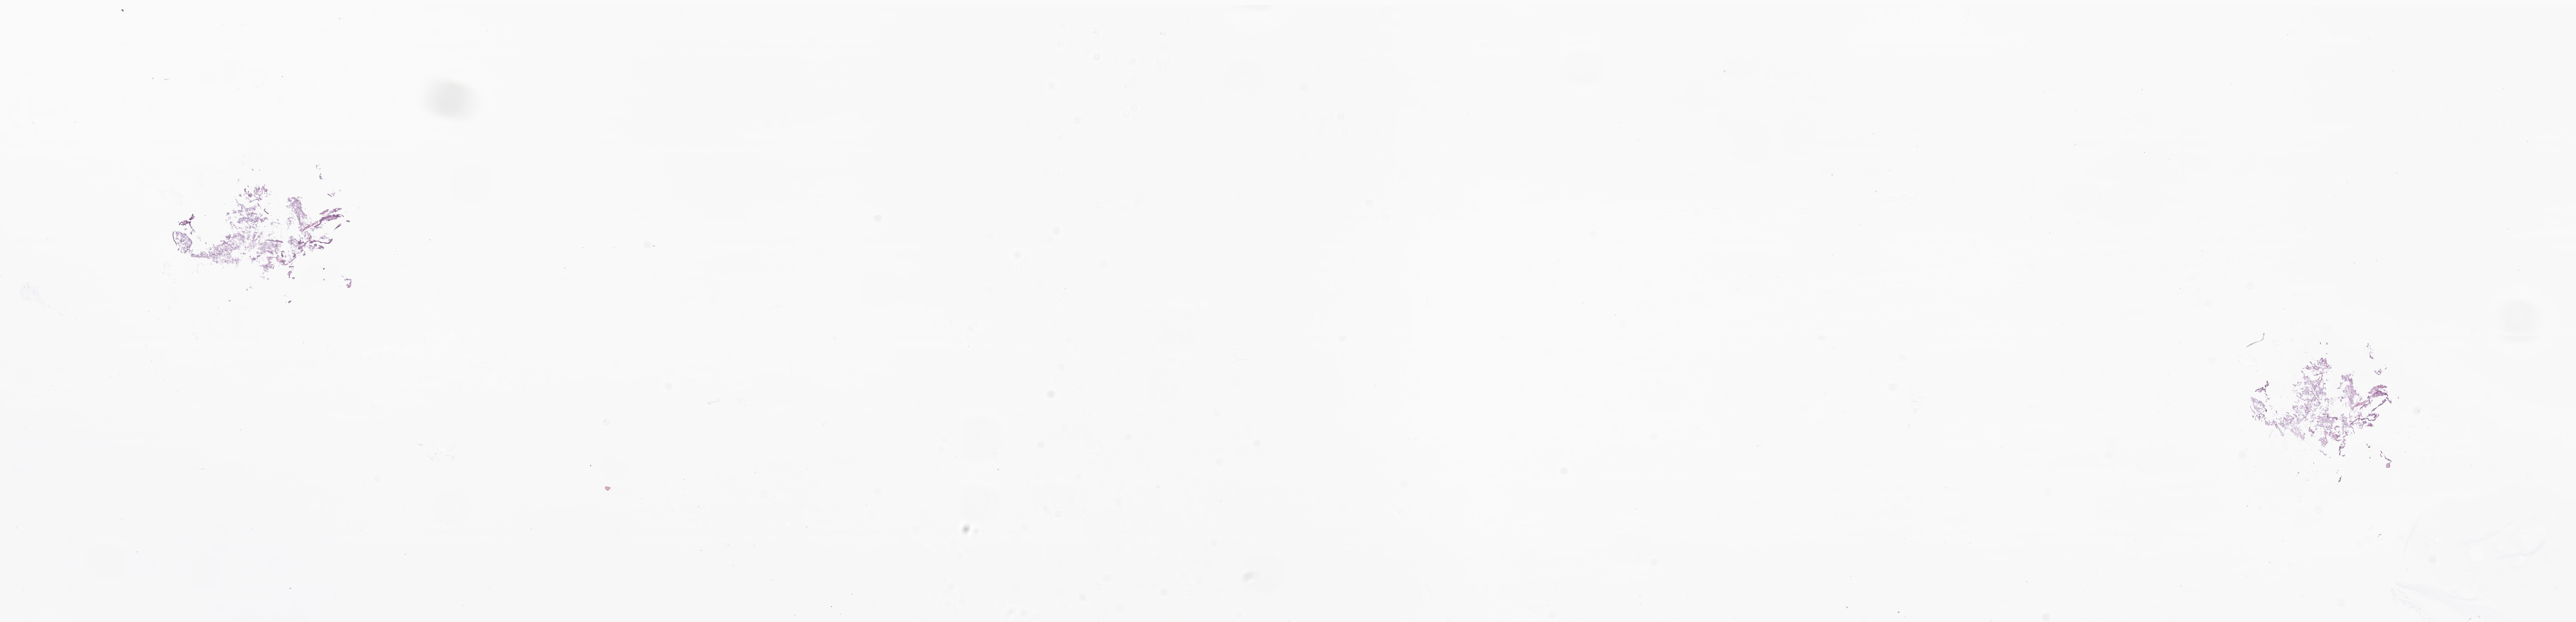
Digitized haematoxylin and eosin-stained section of tumor tissue from the cerebellum — low-resolution overview of the scanned area, about 28.3 x 6.8 mm. Frozen section (OCT-embedded). Male patient, age 101 months.
Diagnosis (ICD-O-3 morphology term): Pilocytic astrocytoma.